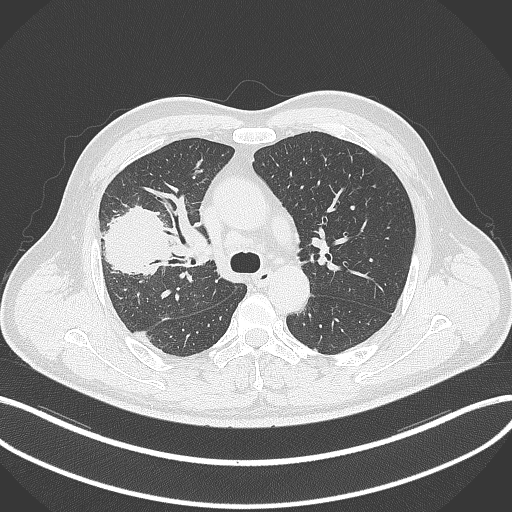
Chest CT, one axial slice. Slice 222 of 348 in the series (ordered by position). 120 kVp. Lung window (W 1500 / L -600 HU). 512 × 512 image matrix, field of view 400 × 400 mm. Patient: male, 55 years. Case-level facts recorded for this patient, not image findings: clinical TNM (as recorded): T3 N2 M1.
Structures marked on this image (bounding box drawn by a radiologist):
- lung tumour (recorded histology: adenocarcinoma): bounding box (x1, y1, x2, y2) in pixels: (99, 205, 171, 278)